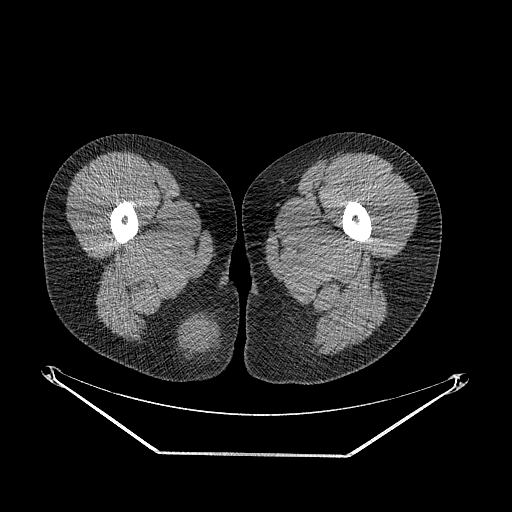
CT of an extremity soft-tissue mass (from a PET/CT study), one axial slice. Slice 19 of 267 in the series (ordered by position). Soft-tissue window (W 400 / L 40 HU). 3.75 mm slice thickness. 512 × 512 image matrix, field of view 500 × 500 mm. Female patient. Case-level facts recorded for this patient, not image findings: histological type: epithelioid sarcoma; grade: intermediate; site of the primary tumour: right buttock.
Outlined on this slice (expert contour drawn on MRI and transferred to this co-registered scan by the dataset authors):
- gross tumour volume including surrounding oedema: bounding box (x1, y1, x2, y2) in pixels: (176, 308, 234, 382)
- gross tumour volume (mass): (180, 317, 220, 352)